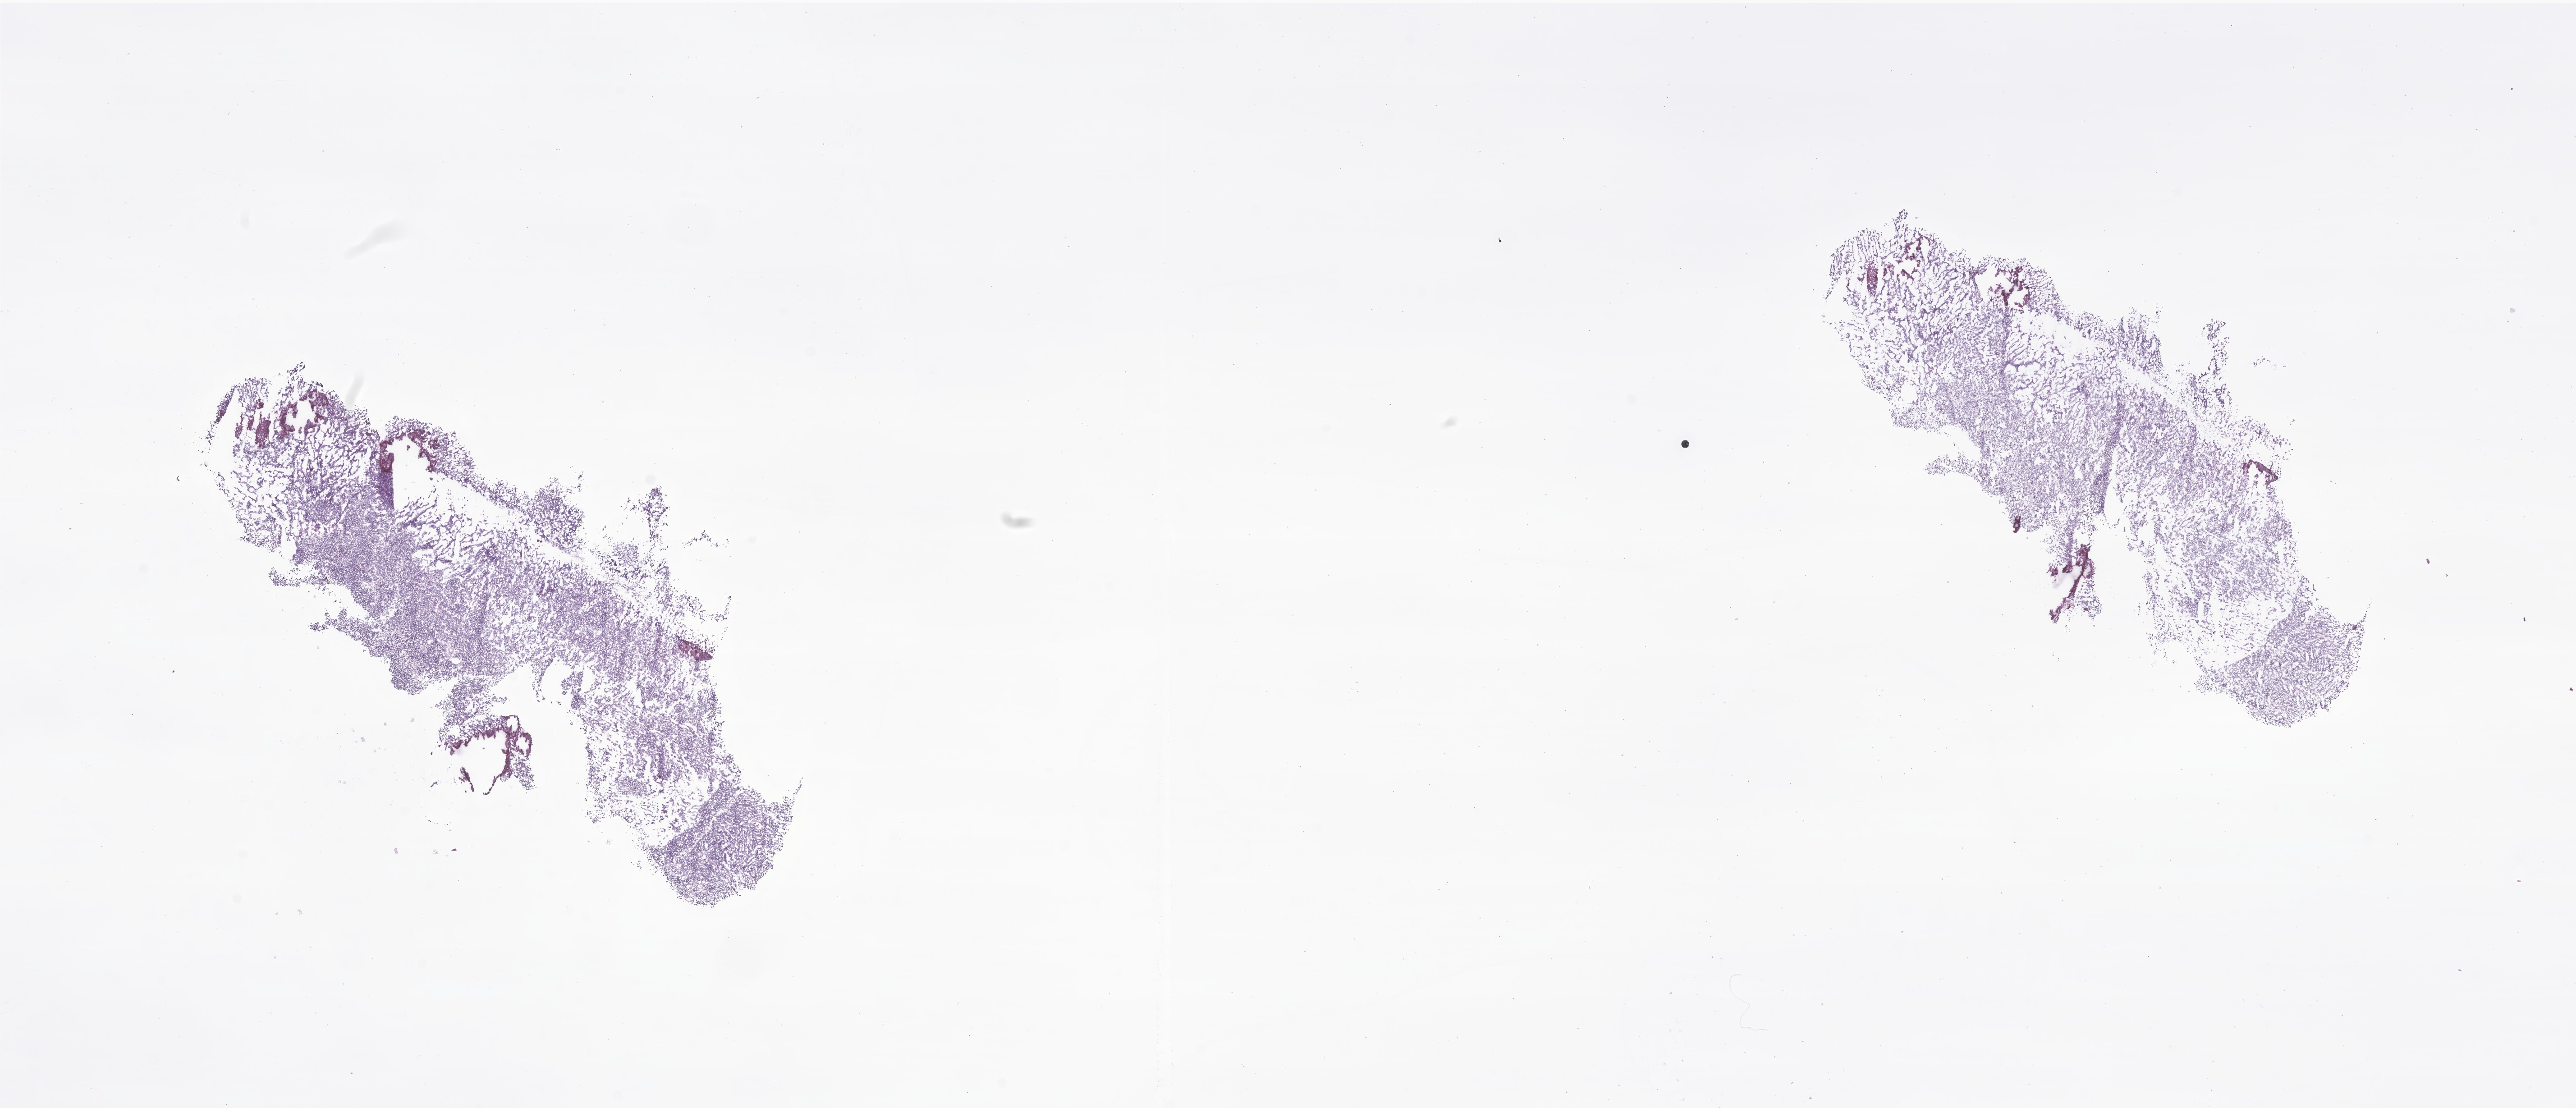
Whole-slide image, H&E stain of tumor tissue from the eye, a low-resolution overview of the entire scanned area, about 24.1 x 10.4 mm. Frozen section. Female patient, age 591 days (about 1.6 years).
Recorded diagnosis: Neoplasm, uncertain whether benign or malignant.